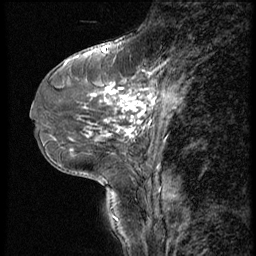
Breast MRI (dynamic contrast-enhanced), one sagittal slice. Slice 23 of 56 in the series (ordered by position). 3 images stored at this slice position (order not interpretable as contrast timing). 1.5 T. TE 4.2 ms, TR 9 ms. 256 × 256 image matrix, field of view 180 × 180 mm. Female patient, age 46 years. Case-level facts recorded for this patient, not image findings: setting: breast cancer imaged before/during neoadjuvant chemotherapy; receptor status: HER2-positive.
Structures marked on this image (semi-automatic segmentation, software-assisted and operator-edited):
- analysis volume of interest (the breast-tissue region the enhancement analysis was run in; not a lesion): bounding box [x1, y1, x2, y2] px = [79, 68, 190, 143]
- tumour enhancement mask (voxels above the 140 % enhancement threshold inside the analysis volume of interest): [88, 73, 171, 138]